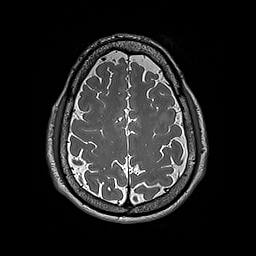
Brain MRI from a brain-tumour surgery series, one axial slice. Slice 66 of 192 in the series (ordered by position). 1 mm slice thickness. 256 × 256 image matrix. From the clinical record (not read from this slice): histopathology: Astrocytoma; WHO grade: 2; IDH mutation: yes.
Annotated regions visible in this slice (manually delineated by an expert):
- tumour: box from (x=159, y=114) to (x=169, y=123) px